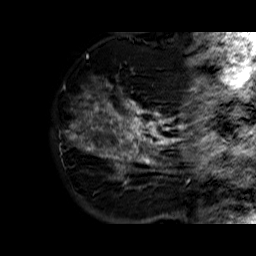
Breast MRI (dynamic contrast-enhanced), one sagittal slice. Position 15 of 60 along the scan axis. Dynamic contrast-enhanced series, time point 2 of 6 at this slice position (early post-contrast). 1.5 T. TE 6.3 ms, TR 32.4 ms. 4 mm slice thickness. 256 × 256 image matrix. Female patient. Case-level facts recorded for this patient, not image findings: setting: breast cancer imaged before/during neoadjuvant chemotherapy; receptor status: HR-positive, HER2-negative.
Outlined on this slice (semi-automatically segmented with operator editing):
- analysis volume of interest (the breast-tissue region the enhancement analysis was run in; not a lesion): bounding box <70,73,177,183> (left, top, right, bottom; pixels)
- tumour enhancement mask (voxels above the 100 % enhancement threshold inside the analysis volume of interest): <75,83,177,183>